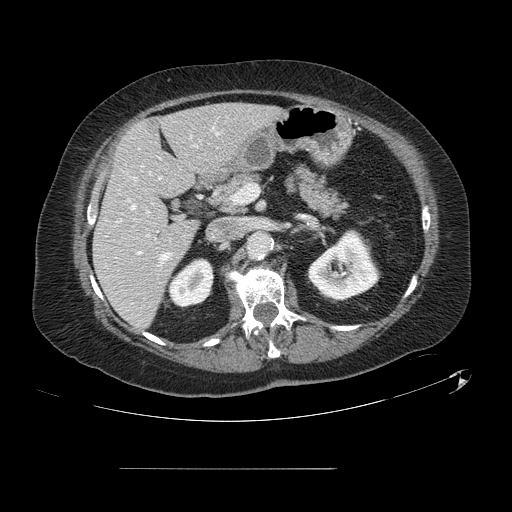
Contrast-enhanced abdominal CT, one axial slice; 120 kVp; soft-tissue window (W 400 / L 40 HU); 2.5 mm slice thickness; 512 × 512 image matrix. Female patient, age 75 years. From the clinical record (not read from this slice): diagnosis: colorectal cancer liver metastases, imaged before liver resection.
Annotated regions visible in this slice (outlined manually by an expert reader):
- hepatic veins: bounding box (x1, y1, x2, y2) in pixels: (128, 132, 218, 261)
- liver: (94, 104, 279, 329)
- planned liver remnant (the part of the liver to remain after resection): (94, 104, 279, 329)
- portal vein (with intrahepatic branches): (138, 211, 149, 255)